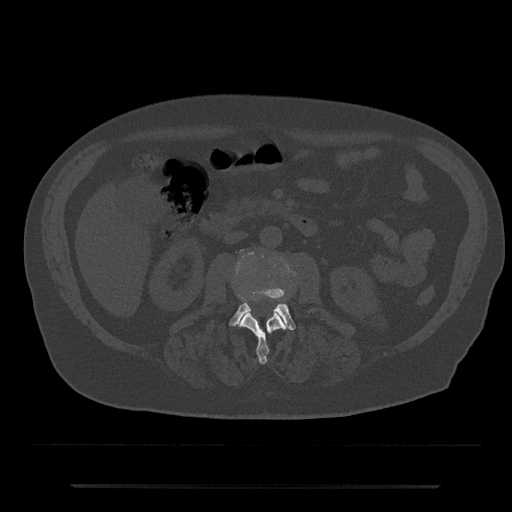
CT including the spine, one axial slice; position 440 of 797 along the scan axis; reconstruction kernel Br40s/3; 120 kVp; bone window (W 1800 / L 400 HU); 0.5 mm slice thickness; 512 × 512 image matrix, field of view 434 × 434 mm. Patient: male, 80 years. From the clinical record (not read from this slice): primary cancer: prostate; vertebrae with lytic lesions (as recorded): L1, T11.
Outlined on this slice (semi-automatically segmented with operator editing):
- L2 vertebra: bounding box [x1, y1, x2, y2] px = [240, 310, 287, 364]
- L3 vertebra: [229, 287, 309, 330]